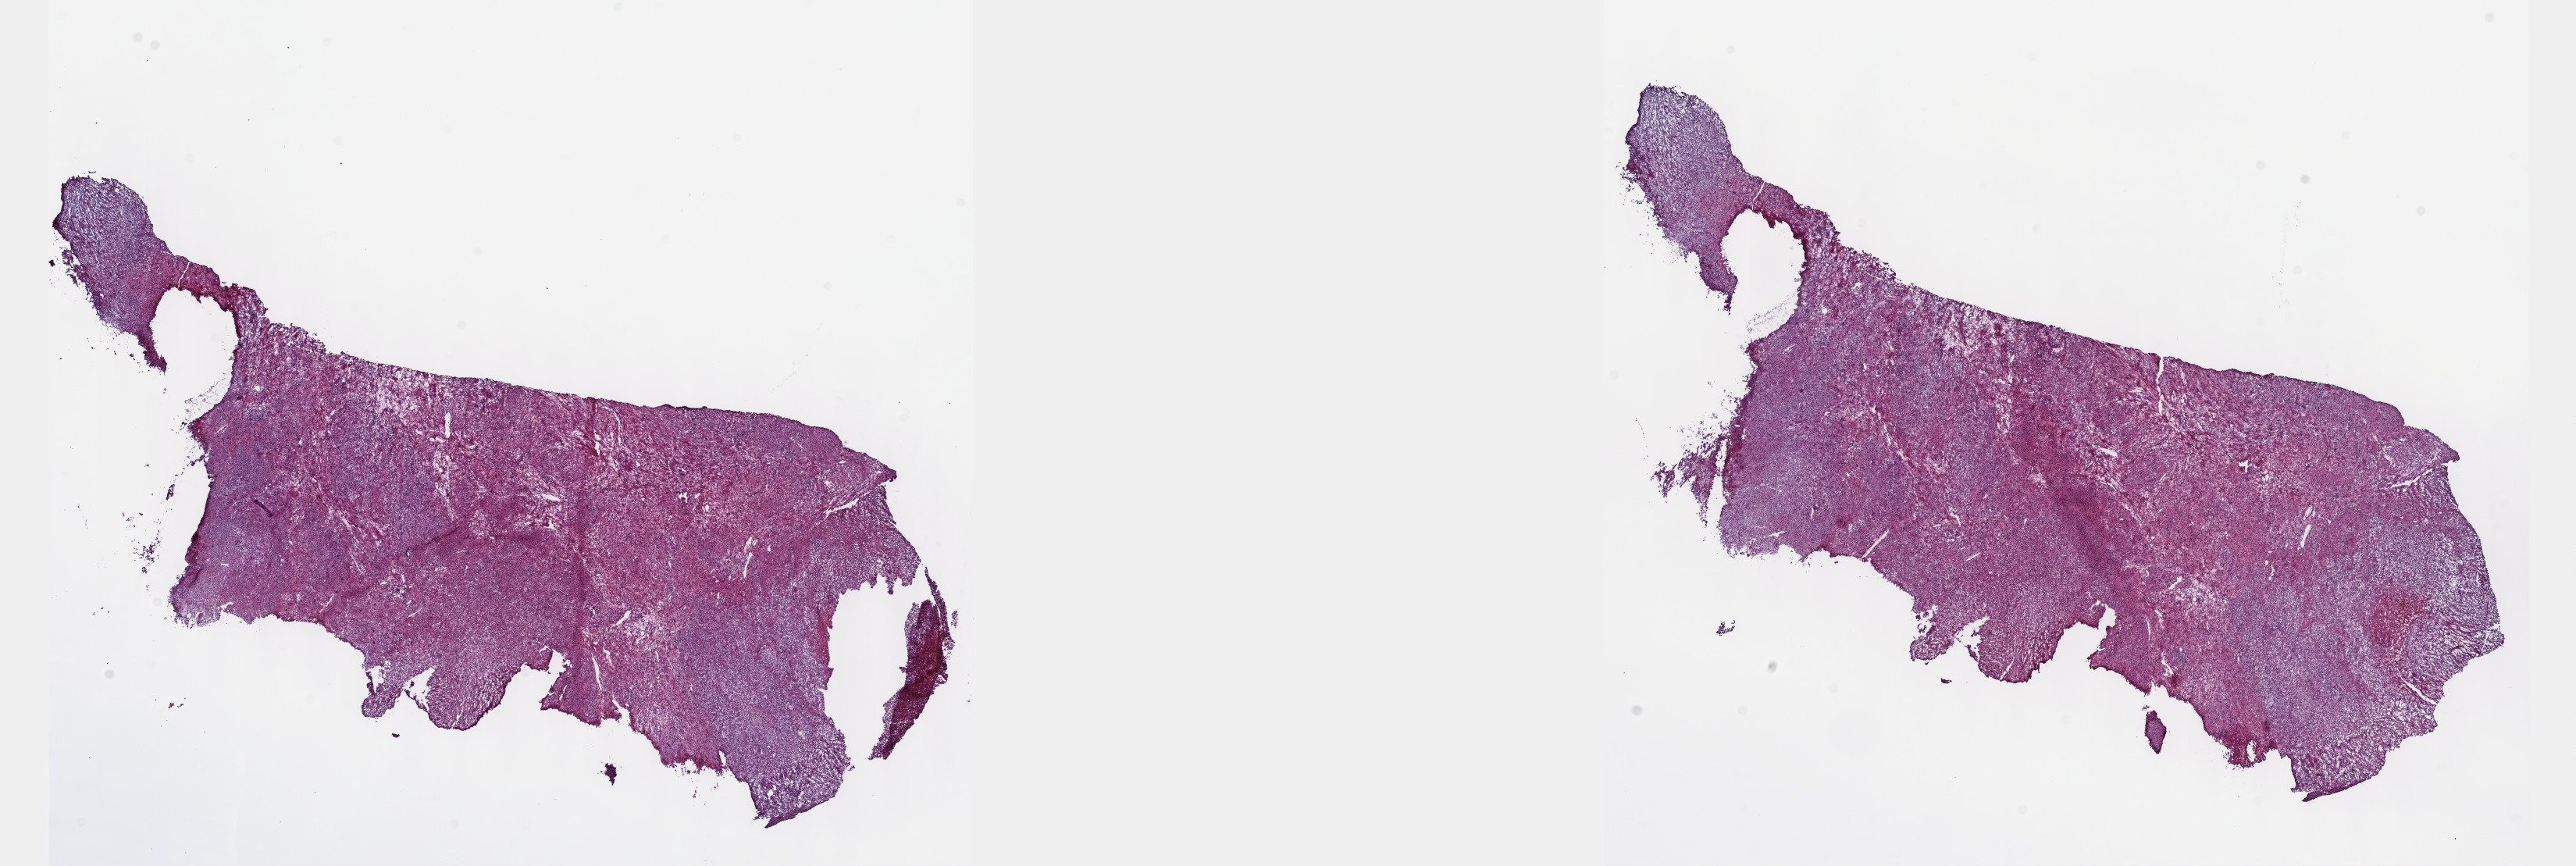
Whole-slide histology image, Hematoxylin and eosin (H&E) stained — low-resolution overview of the scanned area, about 26.7 x 9.0 mm (from a 40x scan); frozen section from the top of the tissue portion; sample: primary tumour, connective, subcutaneous and other soft tissues. Patient: male, age at initial diagnosis 66 years. Composition of this section per pathologist review: tumour cells 100%, tumour nuclei 80%, normal cells 0%, stromal cells 0%, necrosis 0%. Inflammatory infiltration, as recorded: lymphocyte infiltration 1%, monocyte infiltration 0%, neutrophil infiltration 0%.
Diagnosis: Leiomyosarcoma, NOS.